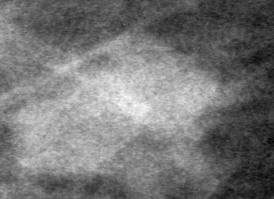
Crop from a digitized film mammogram around one marked abnormality; right breast; CC view.
Marked abnormality: mass, shape lobulated, margins ill defined; BI-RADS assessment category 4; subtlety rating 3 on a 1 (subtle) to 5 (obvious) scale; pathology (as recorded): malignant.